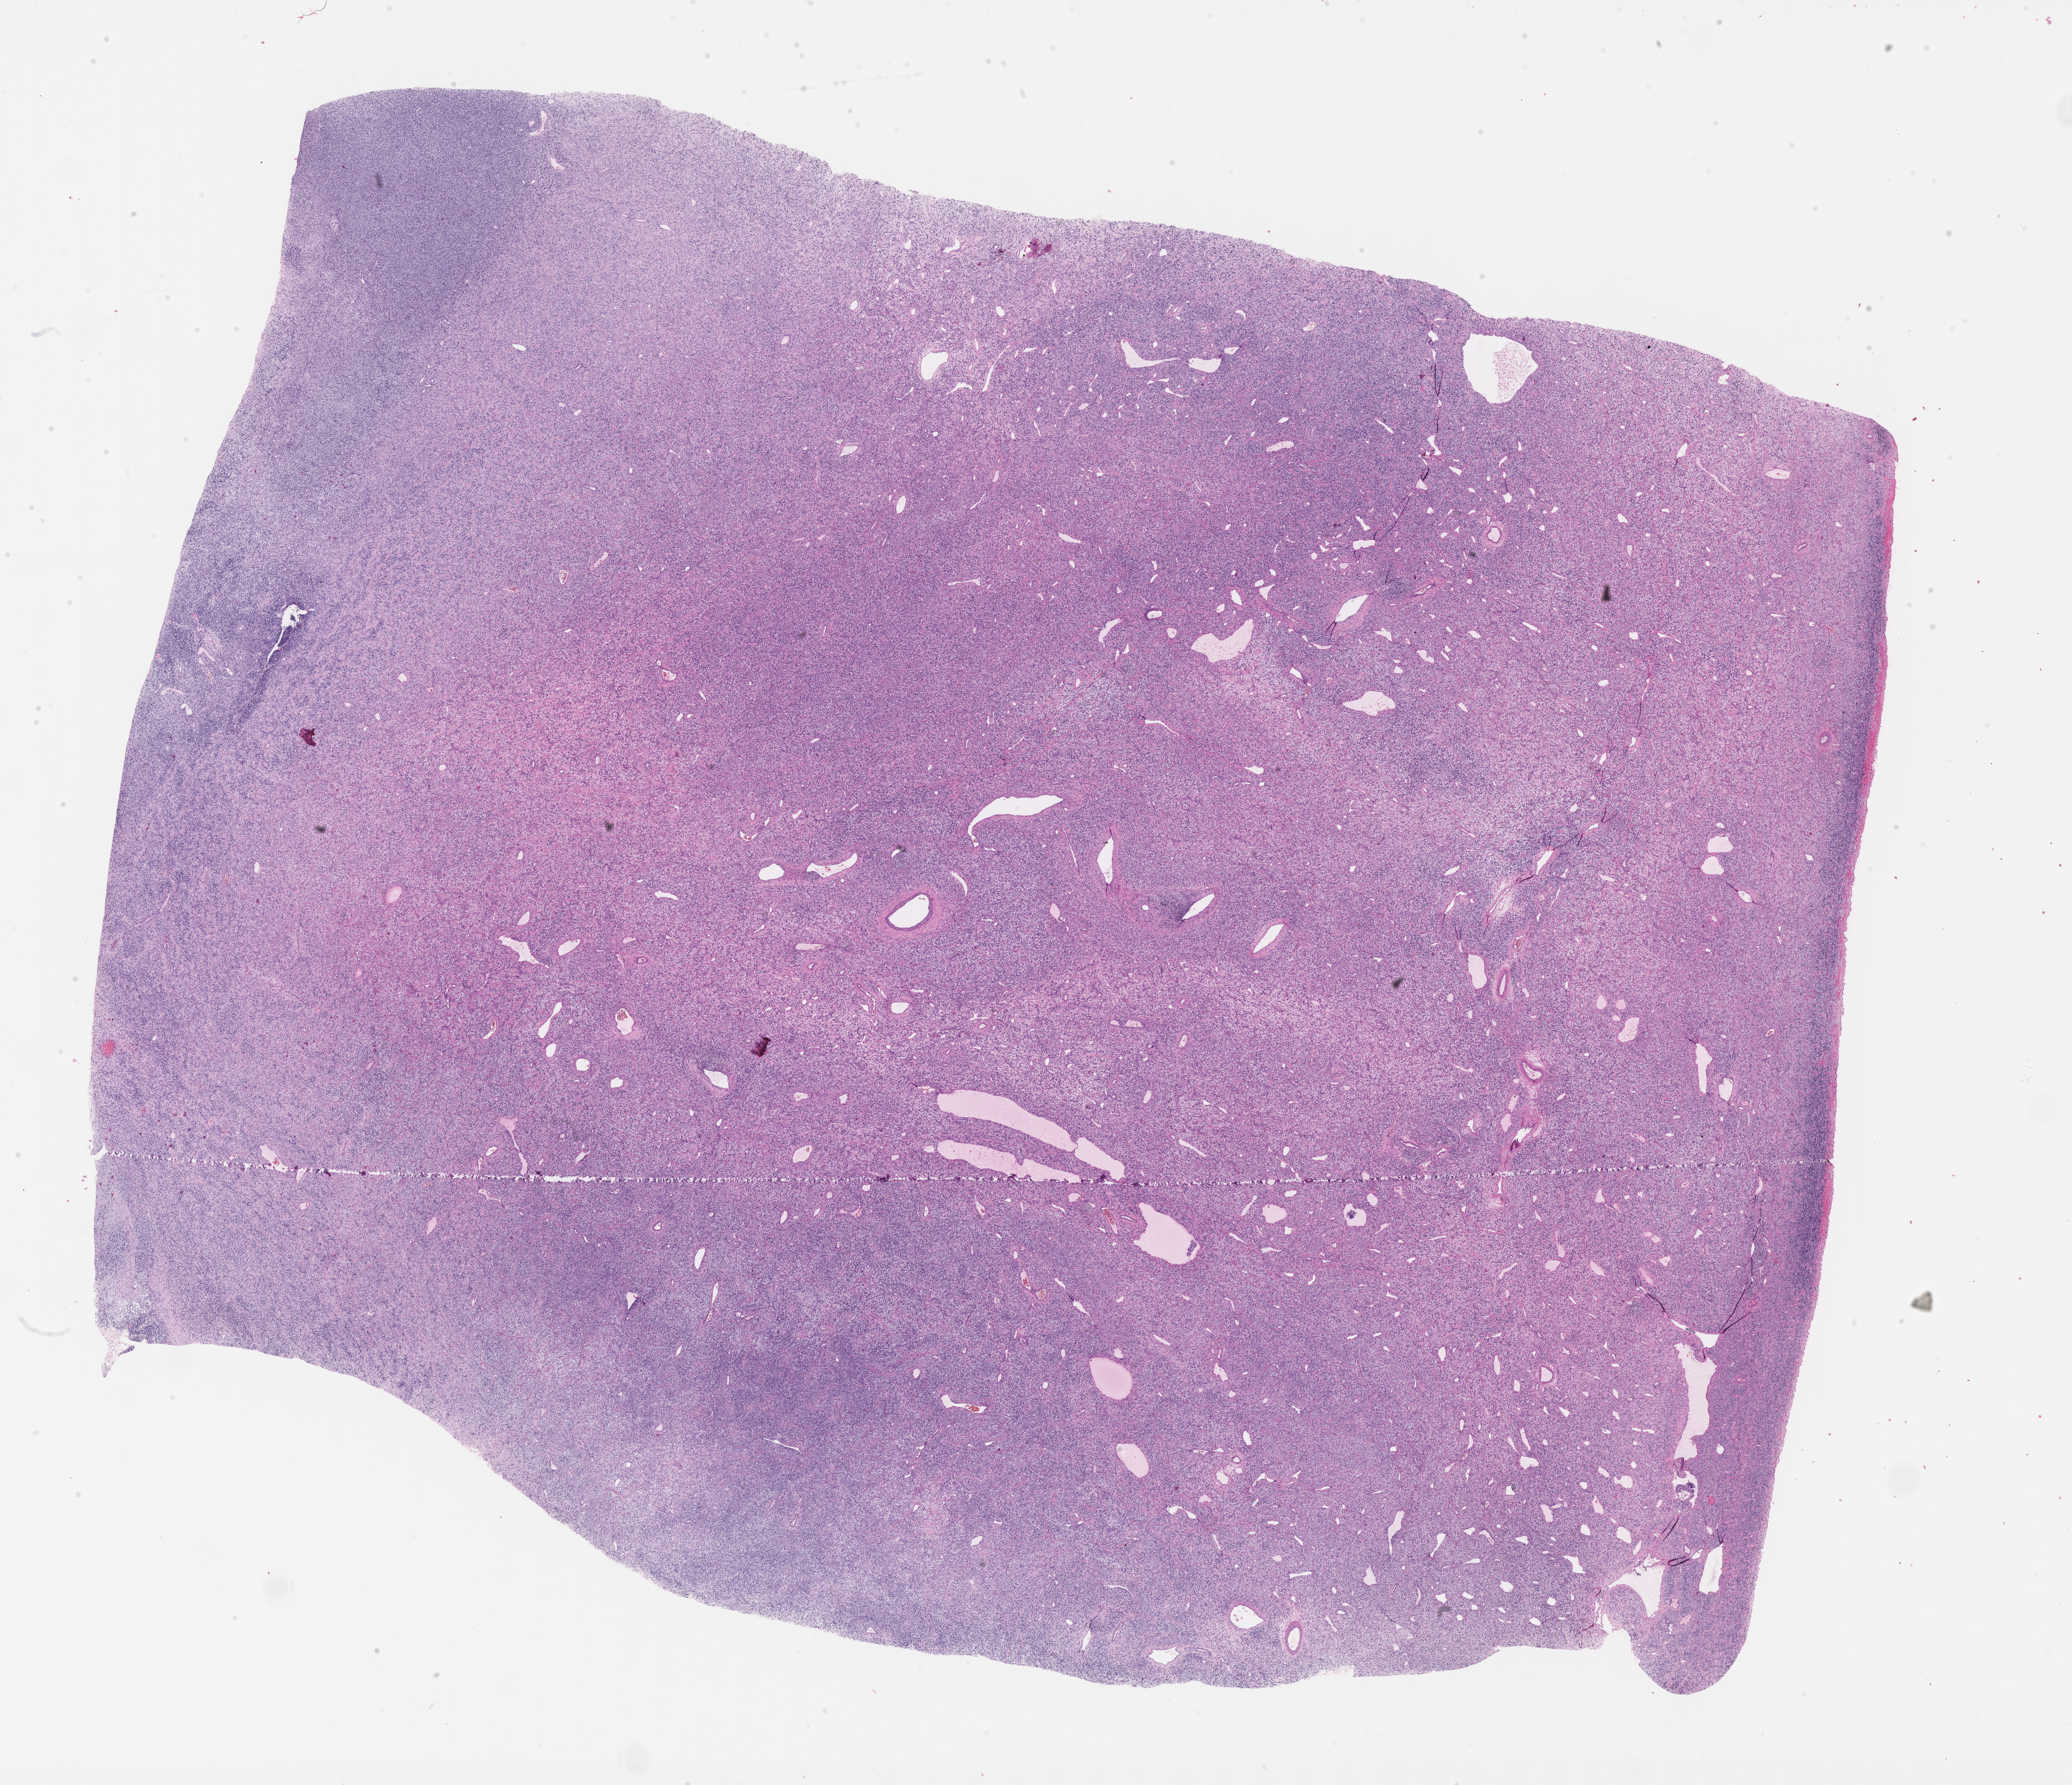
Whole-slide image, haematoxylin and eosin stain of tumor tissue, shown as a low-resolution overview of the whole scanned area (about 25.2 x 21.7 mm). FFPE section. Sample anatomic site: scrotum, right. Male patient, age at diagnosis 9.8 years.
- stage (as recorded): 1
- diagnosis: rhabdomyosarcoma; histological classification: embryonal rhabdomyosarcoma
- metastatic status at presentation (as recorded): non-metastatic